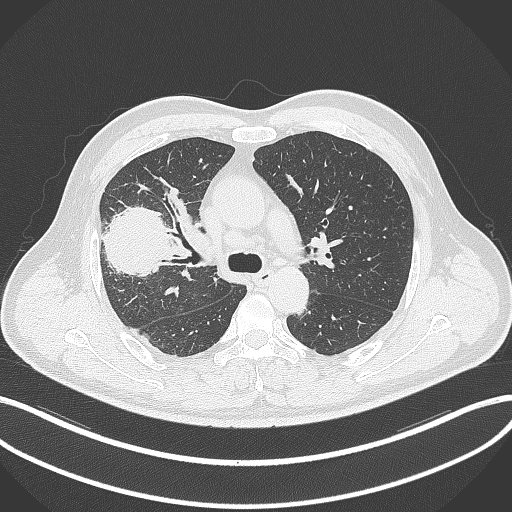
Chest CT, one axial slice. Position 219 of 348 along the scan axis. 120 kVp. Lung window (W 1500 / L -600 HU). 1 mm slice thickness. 512 × 512 image matrix. Male patient, age 55 years. Case-level facts recorded for this patient, not image findings: clinical TNM (as recorded): T3 N2 M1.
Annotated regions visible in this slice (rectangle marked by the reading radiologist):
- lung tumour (recorded histology: adenocarcinoma): bounding box (x1, y1, x2, y2) in pixels: (98, 204, 171, 279)